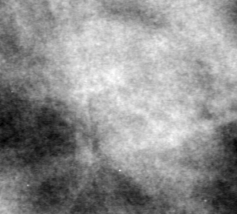
Cropped region of a digitized screen-film mammogram centred on a radiologist-marked abnormality, right breast, MLO view, BI-RADS breast density category 2 (scale 1–4).
Mass, shape lobulated, margins ill defined; BI-RADS assessment category 4; subtlety rating 1 on a 1 (subtle) to 5 (obvious) scale; pathology result (as recorded, not read from the image): benign.